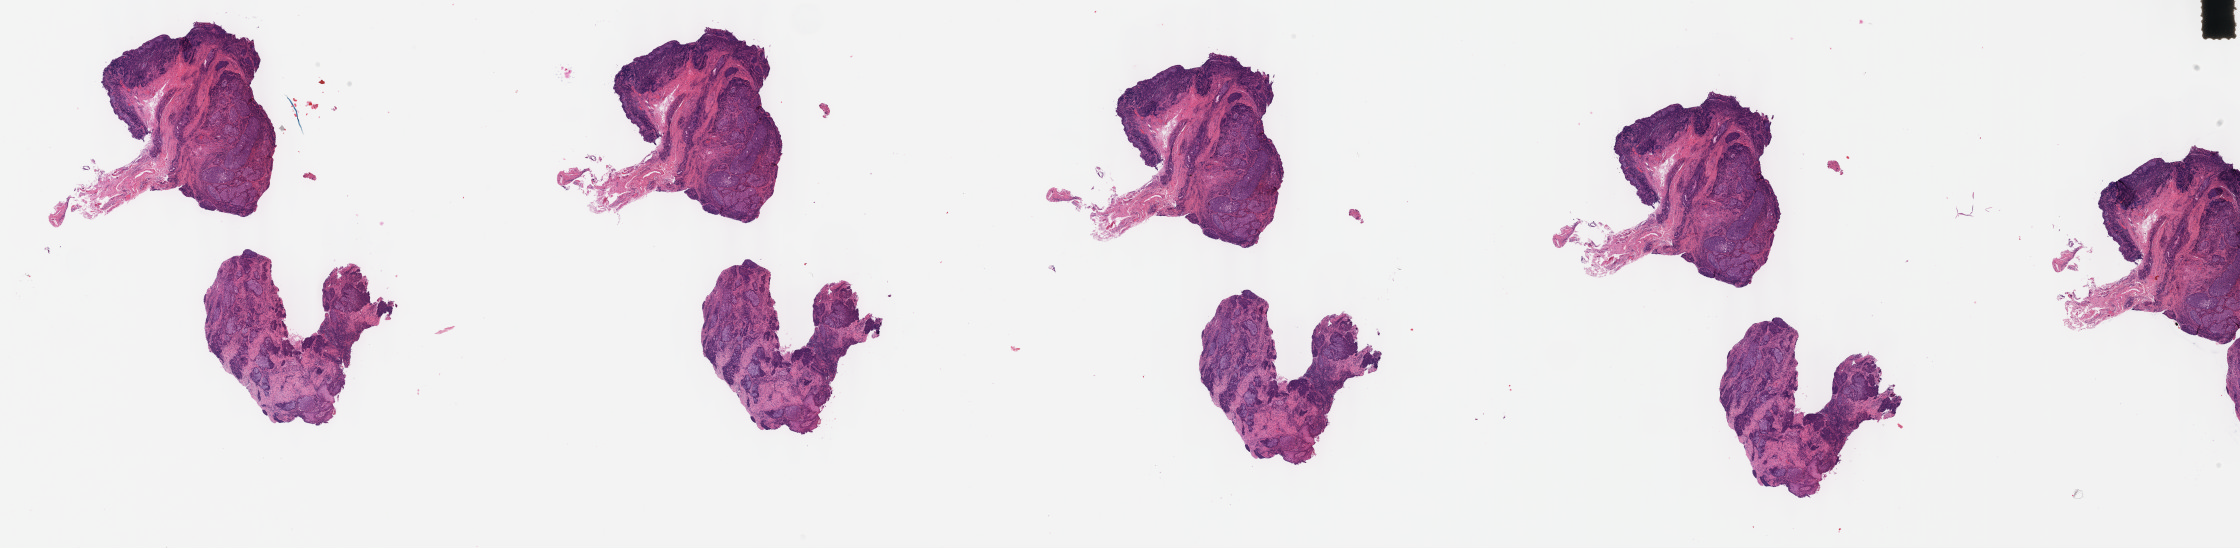
Whole-slide histology image, H&E, a low-resolution overview of the entire scanned area, about 36.2 x 8.9 mm (slide scanned at 40x), FFPE section, primary tumour sample from the head and neck. Male patient; age at initial diagnosis 68 years. Histologic grade: G2 (moderately differentiated).
* histologic diagnosis: Squamous cell carcinoma, NOS (oropharynx, NOS)